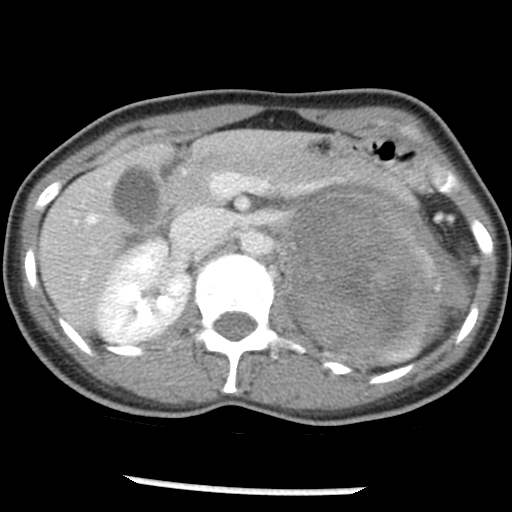
Contrast-enhanced abdominal CT, one axial slice; position 27 of 54 along the scan axis; 120 kVp; soft-tissue window (W 400 / L 40 HU); 5 mm slice thickness; 512 × 512 image matrix, field of view 240 × 240 mm. Patient: female, 33 years. Case-level facts recorded for this patient, not image findings: diagnosis: adrenocortical carcinoma; tumour side: left adrenal; tumour size at pathology: 11 cm; Ki-67 index: 20 %; stage (as recorded): 2.
Annotated regions visible in this slice (semi-automatic segmentation, software-assisted and operator-edited):
- mass: box from (x=281, y=188) to (x=465, y=362) px